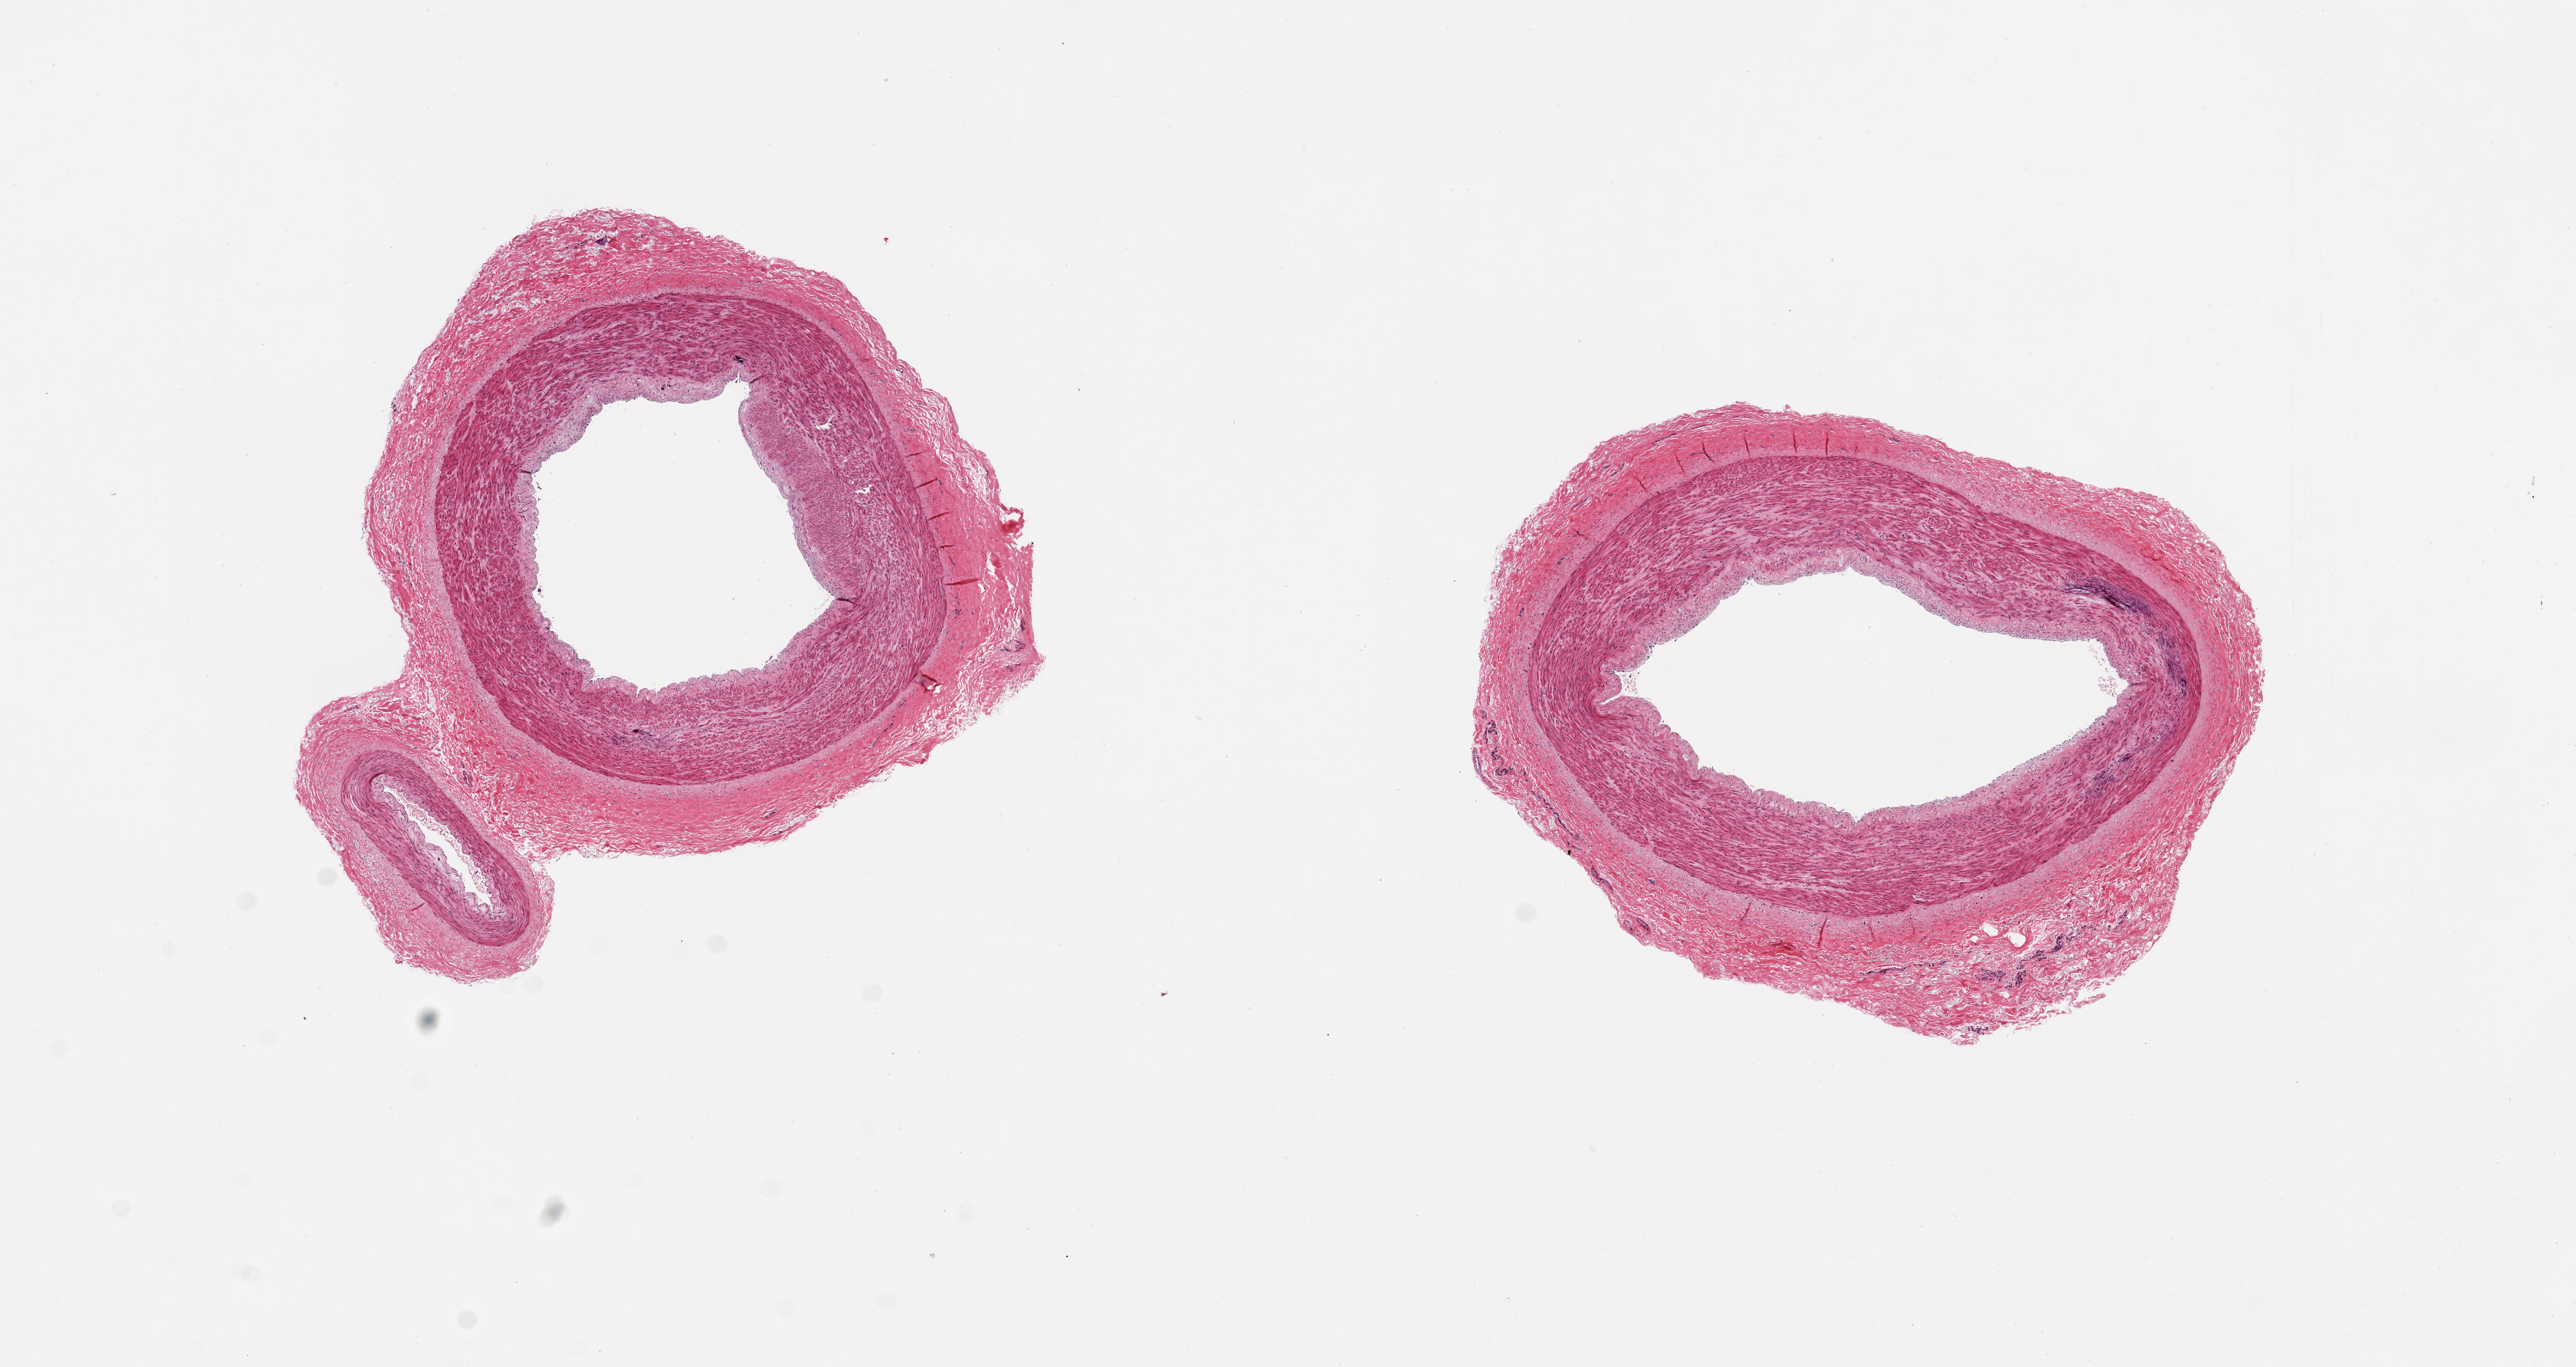
H&E whole-slide image, whole scanned area (about 14.8 x 7.8 mm) shown as a low-resolution overview. PAXgene-fixed, paraffin-embedded tissue. Section of tibial artery (target tissue). Donor tissue sample.
Review note (as recorded): 2 pieces. 4x3 & 5x4mm; Well dissected.